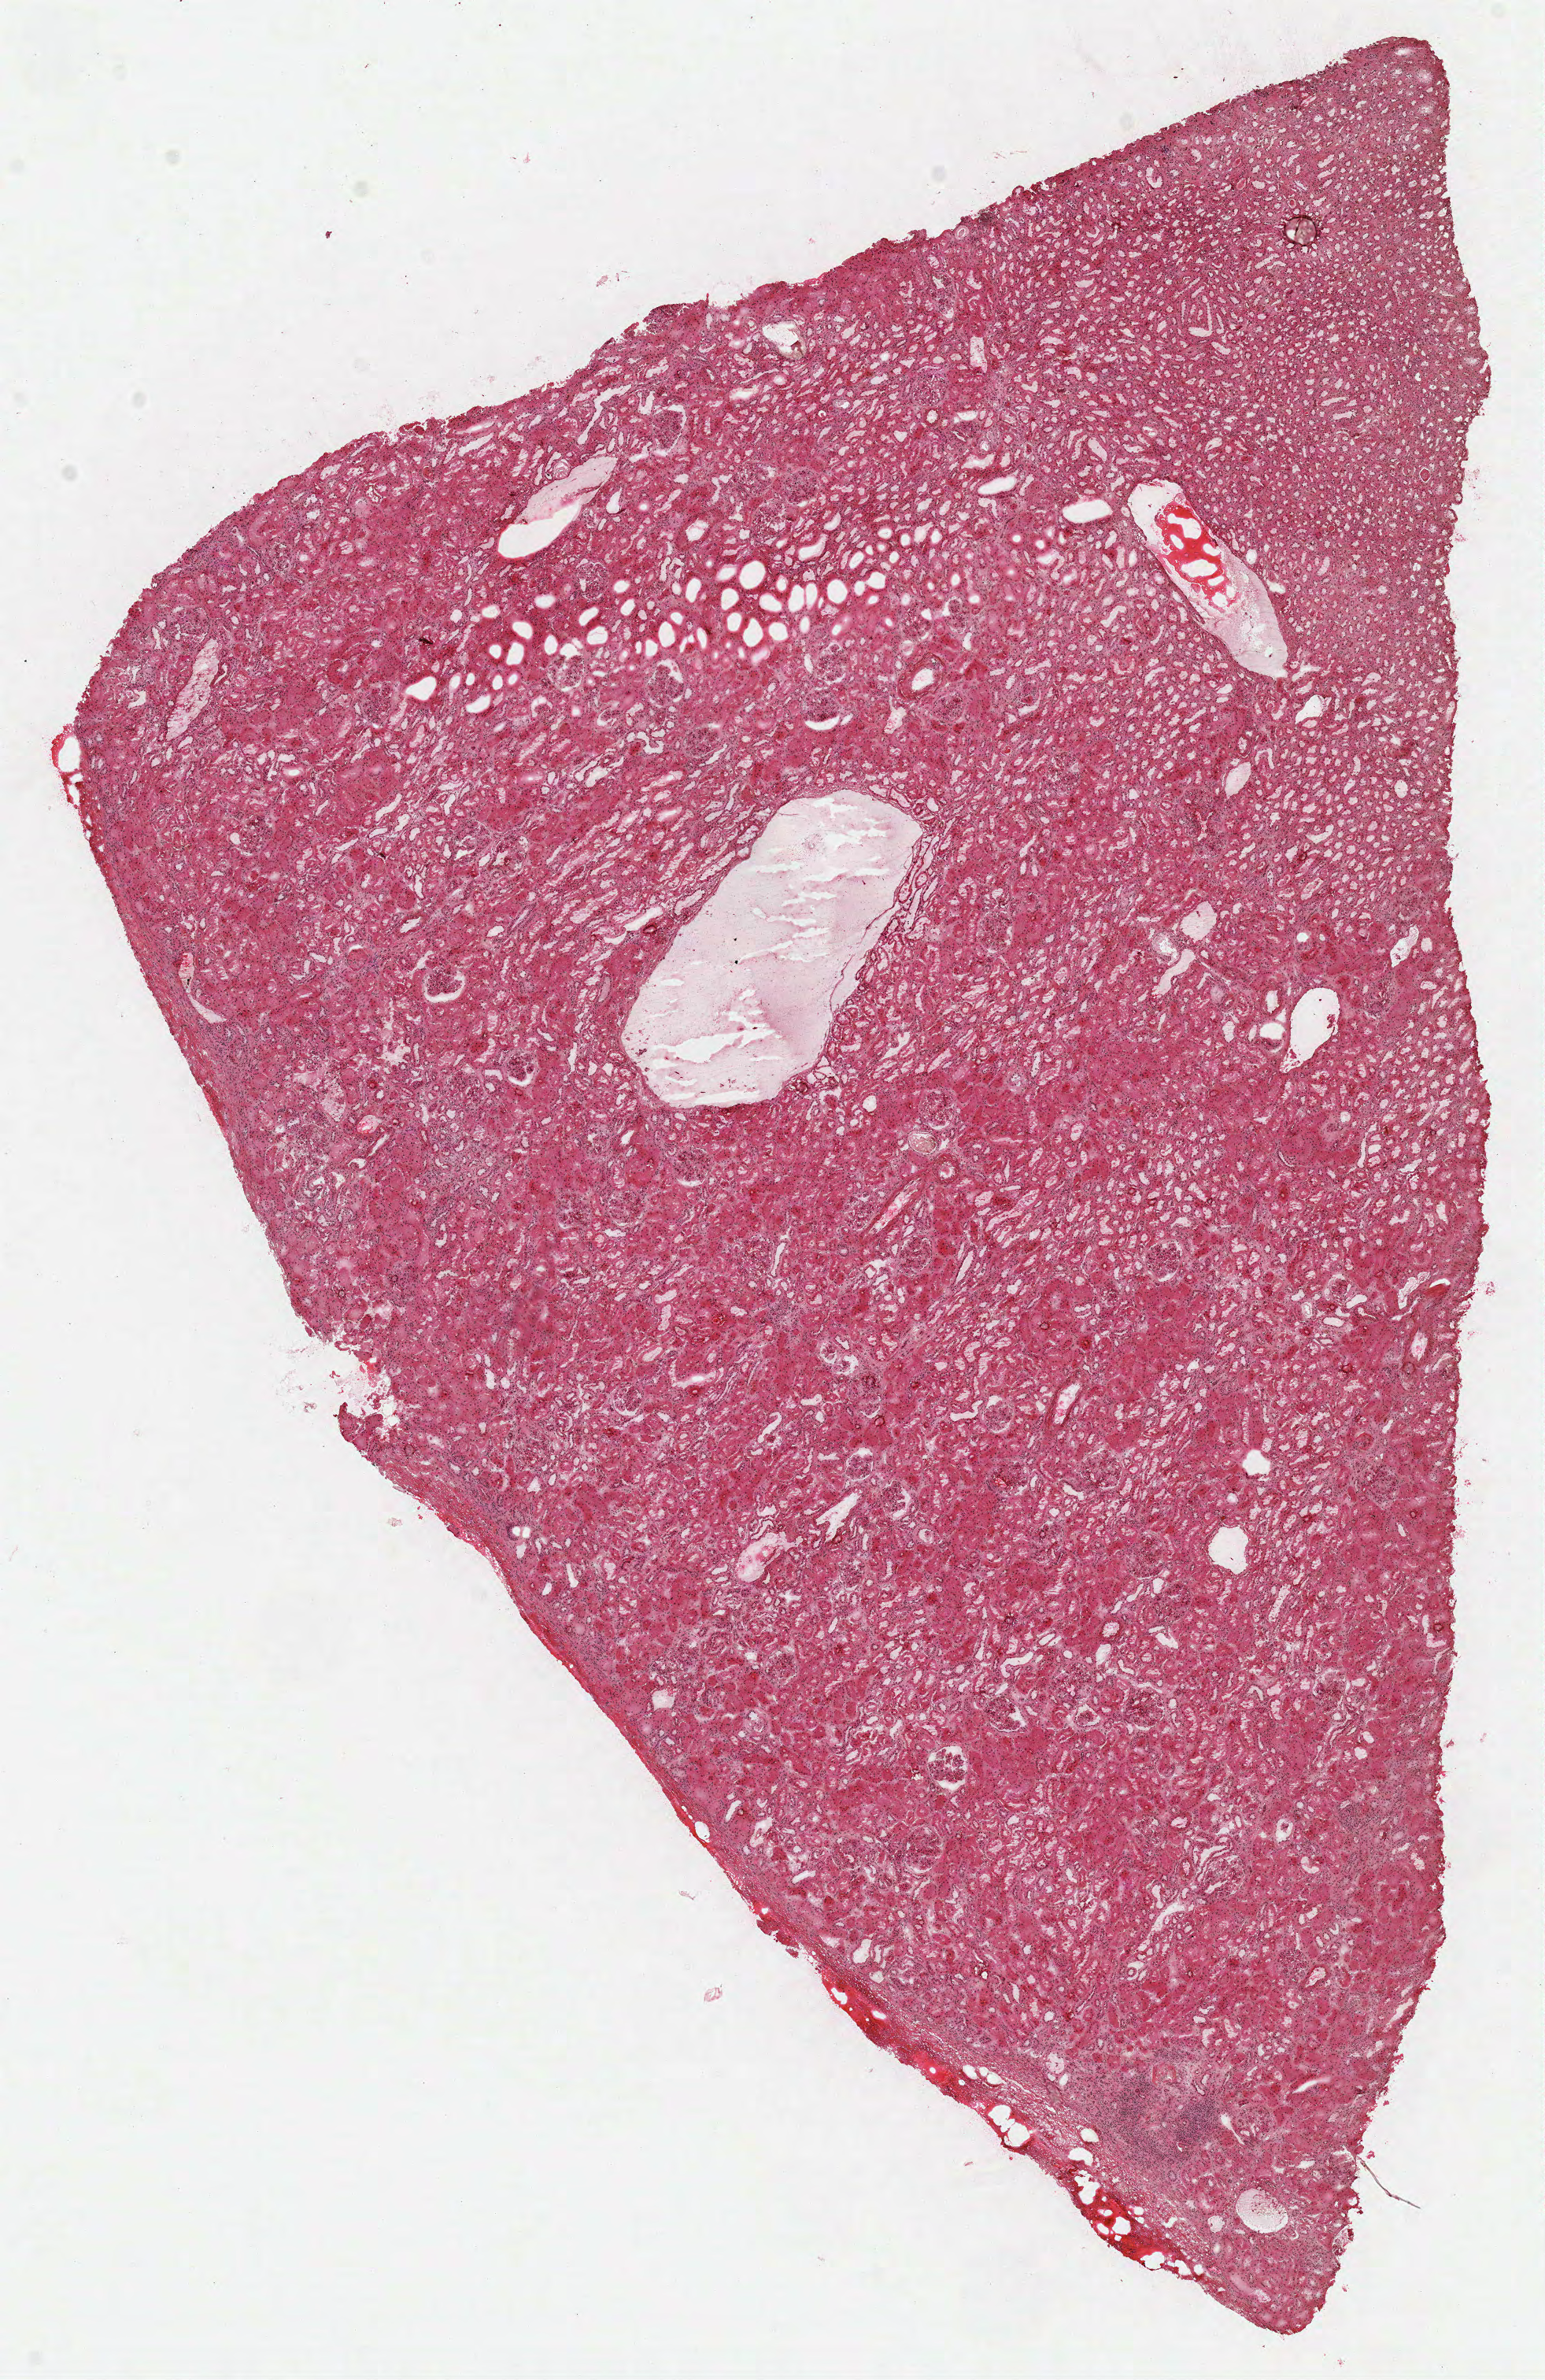
Hematoxylin and eosin (H&E) stained whole-slide image, low-resolution overview of the scanned area, about 7.7 x 11.9 mm. Frozen section from the top of the tissue portion. Sample: solid tissue normal (non-tumour tissue), kidney. Female, age 79 years at initial diagnosis.
This section: solid tissue normal (non-tumour) sample from the same patient. Patient diagnosis: Papillary adenocarcinoma, NOS.